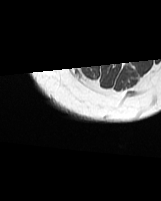
MRI of an extremity soft-tissue mass, one axial slice; MR volume resampled by the dataset authors to the PET/CT grid (not the native acquisition matrix); 3.27 mm slice thickness; 161 × 201 image matrix. Female patient. From the clinical record (not read from this slice): histological type: synovial sarcoma; grade: intermediate; site of the primary tumour: right buttock.
Outlined on this slice (expert contour drawn on MRI and transferred to this co-registered scan by the dataset authors):
- gross tumour volume including surrounding oedema: bounding box [x1, y1, x2, y2] px = [72, 68, 82, 80]